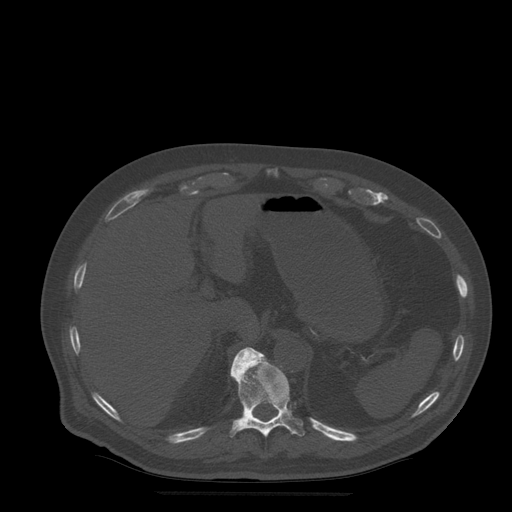
CT including the spine, one axial slice; slice 245 of 522 in the series (ordered by position); bone window (W 1800 / L 400 HU); 512 × 512 image matrix, field of view 420 × 420 mm. Patient age 72 years. Case-level facts recorded for this patient, not image findings: primary cancer: prostate.
Outlined on this slice (semi-automatic segmentation, software-assisted and operator-edited):
- T11 vertebra: bounding box <230,347,305,438> (left, top, right, bottom; pixels)